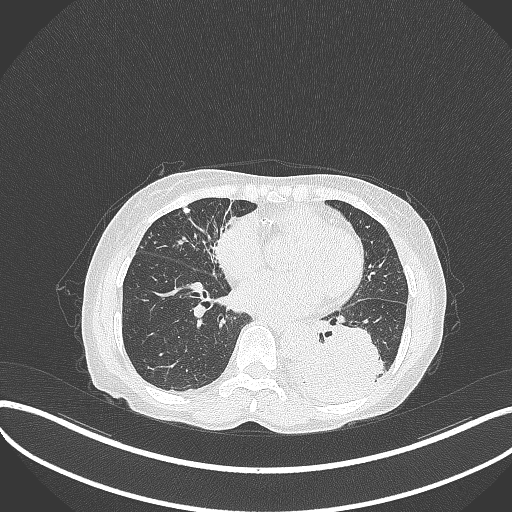
Chest CT, one axial slice; slice 124 of 370 in the series (ordered by position); 120 kVp; lung window (W 1500 / L -600 HU); 1 mm slice thickness; 512 × 512 image matrix, field of view 400 × 400 mm. Female patient, age 78 years. From the clinical record (not read from this slice): clinical TNM (as recorded): T3 N0 M1.
Annotated regions visible in this slice (rectangle marked by the reading radiologist):
- lung tumour (recorded histology: squamous cell carcinoma): bounding box [x1, y1, x2, y2] px = [290, 321, 385, 404]